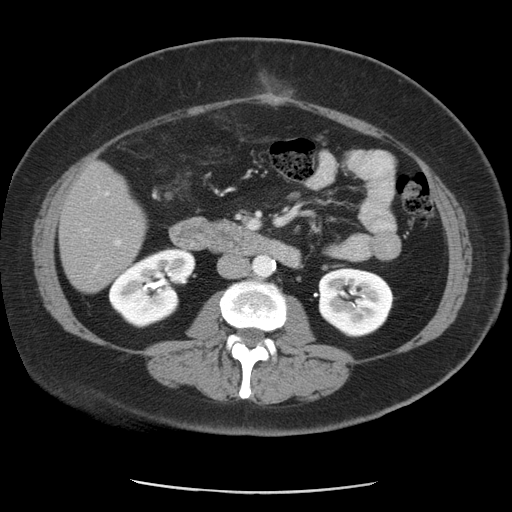
Contrast-enhanced abdominal CT, one axial slice. Slice 13 of 55 in the series (ordered by position). 120 kVp. Intravenous contrast given. Soft-tissue window (W 400 / L 40 HU). 5 mm slice thickness. 512 × 512 image matrix. Female patient, age 52 years. Case-level facts recorded for this patient, not image findings: diagnosis: colorectal cancer liver metastases, imaged before liver resection; multiple liver metastases: yes; largest metastasis: 2.5 cm; disease in both lobes: yes.
Annotated regions visible in this slice (expert manual segmentation):
- liver: box from (x=59, y=163) to (x=148, y=293) px
- planned liver remnant (the part of the liver to remain after resection): (x=60, y=193)–(x=137, y=293)
- portal vein (with intrahepatic branches): (x=80, y=184)–(x=123, y=272)